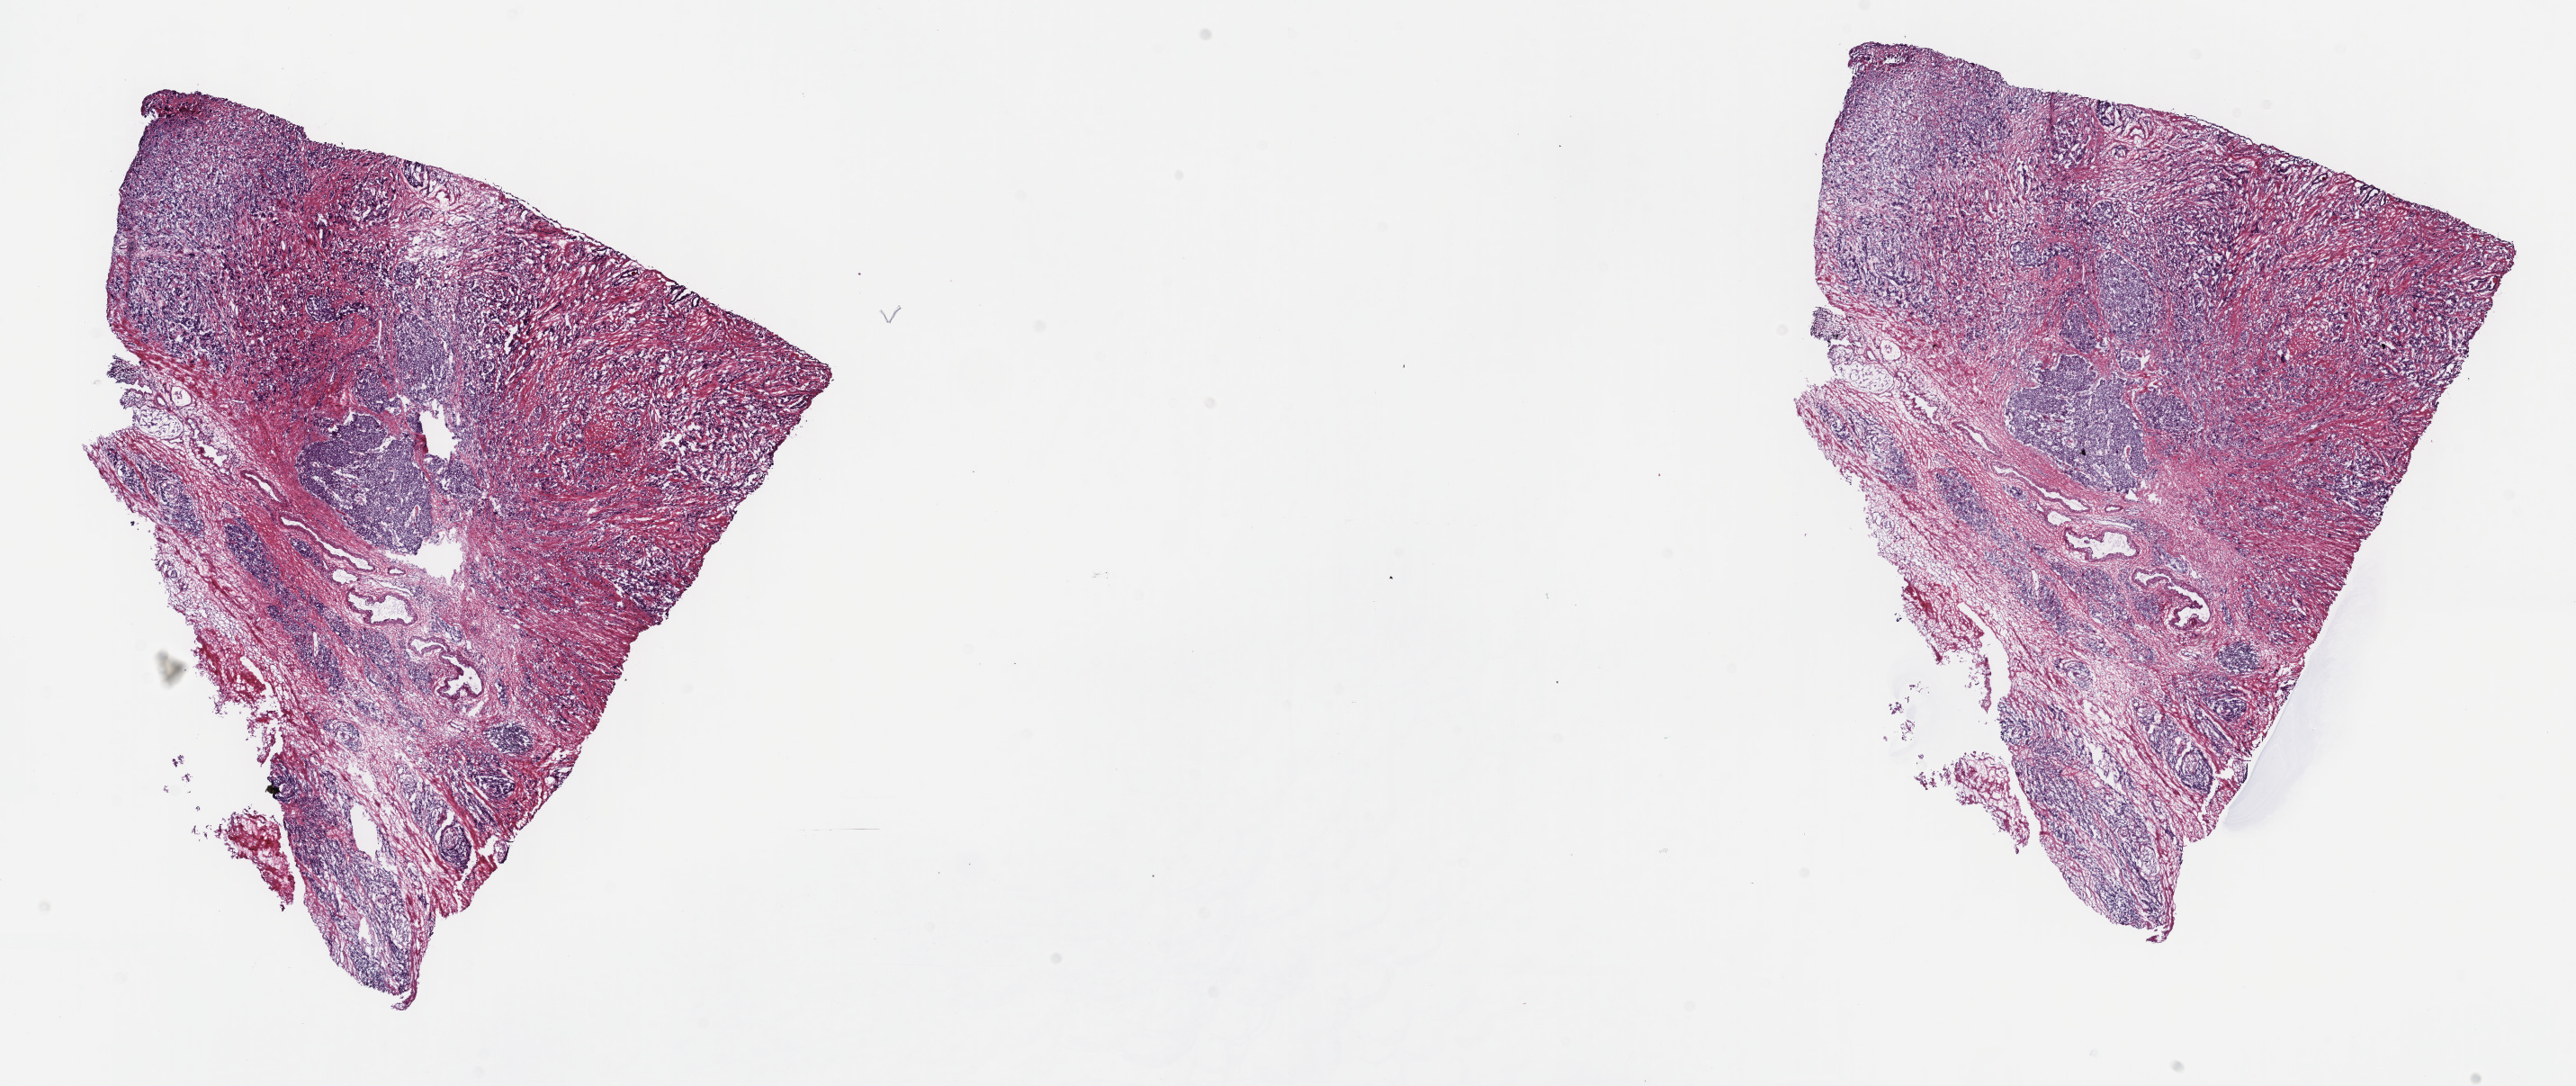
Digitized H&E-stained tissue section (whole slide) — whole scanned area (about 23.2 x 9.8 mm, from a 40x scan) shown as a low-resolution overview; frozen section from the top of the tissue portion; sample: primary tumour, prostate. Male patient; age at initial diagnosis 54 years. Gleason score: 9 (5+4). Pathologist review of this section (percent, as recorded): tumour cells 90%, tumour nuclei 75%, normal cells 0%, stromal cells 10%, necrosis 0%. Infiltration values recorded for this section: lymphocyte infiltration 0%, monocyte infiltration 0%, neutrophil infiltration 0%.
Lymph nodes positive (case pathology): 0 of 10 examined. Histologic diagnosis: Adenocarcinoma, NOS (prostate gland).